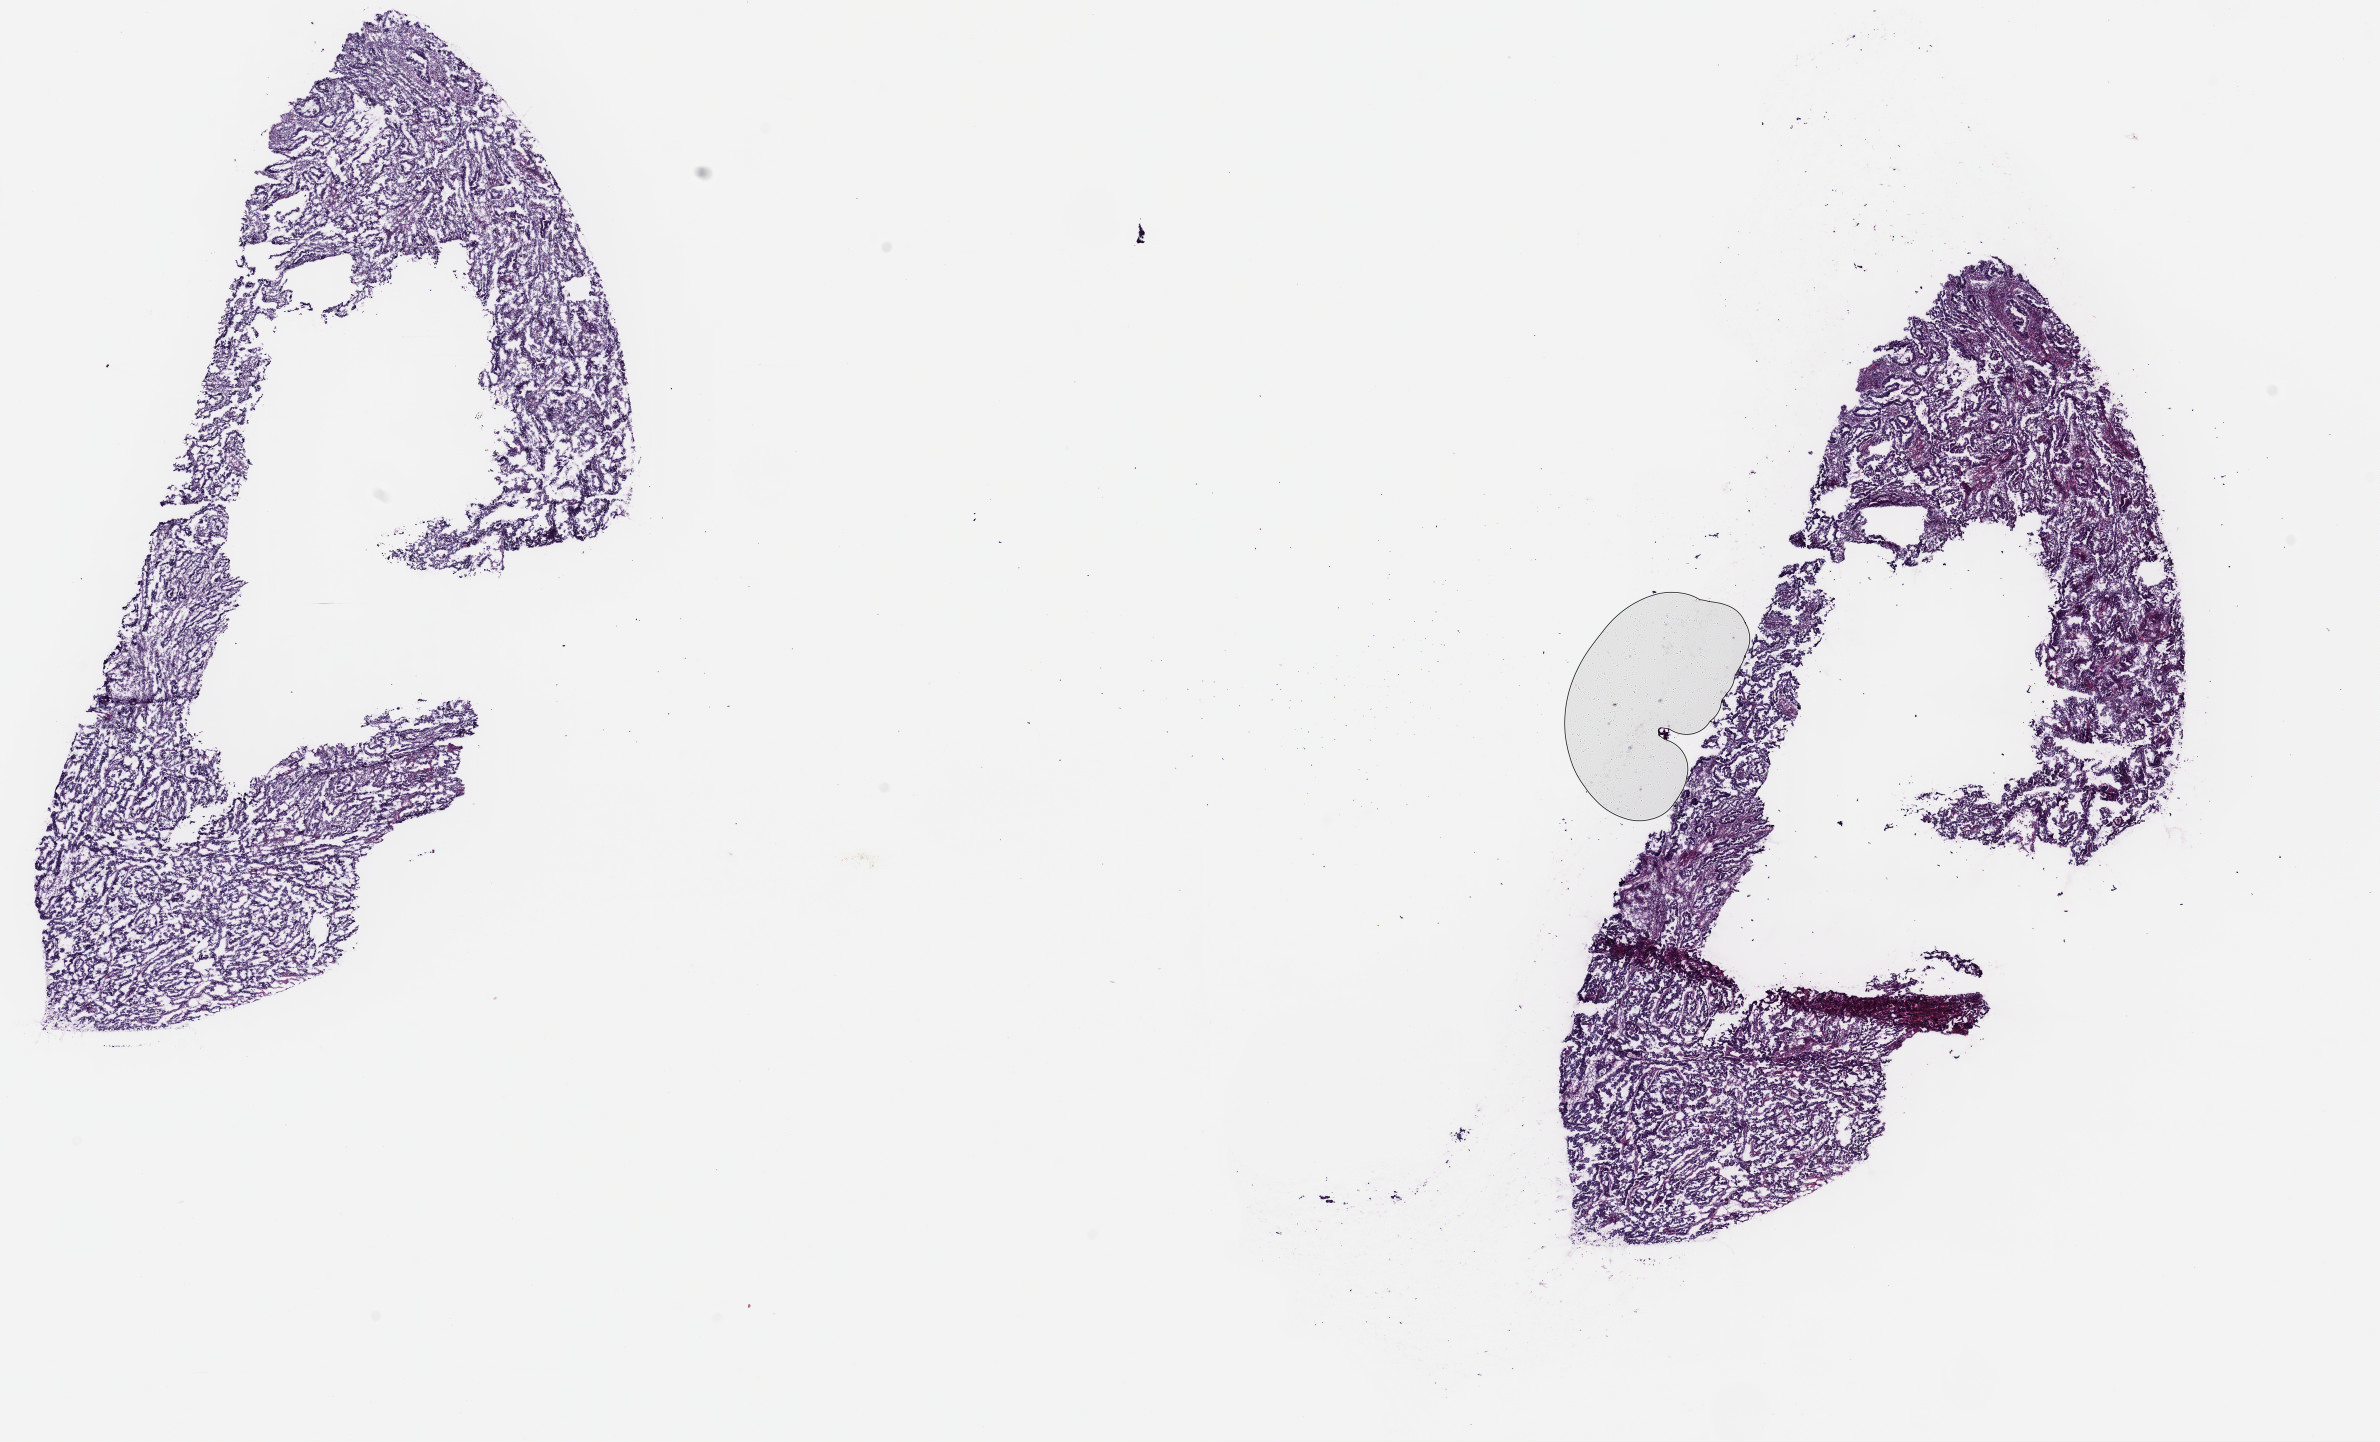
Hematoxylin and eosin (H&E) stained whole-slide image — shown as a low-resolution overview of the whole scanned area (about 18.8 x 11.4 mm); frozen section from the top of the tissue portion; uterus, primary tumour sample. Patient: female, age at initial diagnosis 64 years. Histologic grade: G3 (poorly differentiated). Pathologist review of this section (percent, as recorded): tumour cells 90%, tumour nuclei 90%, normal cells 0%, stromal cells 5%, necrosis 5%. Inflammatory infiltration, as recorded: lymphocyte infiltration 40%, monocyte infiltration 20%, neutrophil infiltration 20%.
FIGO stage: IIB. Histologic diagnosis: Serous cystadenocarcinoma, NOS (endometrium).